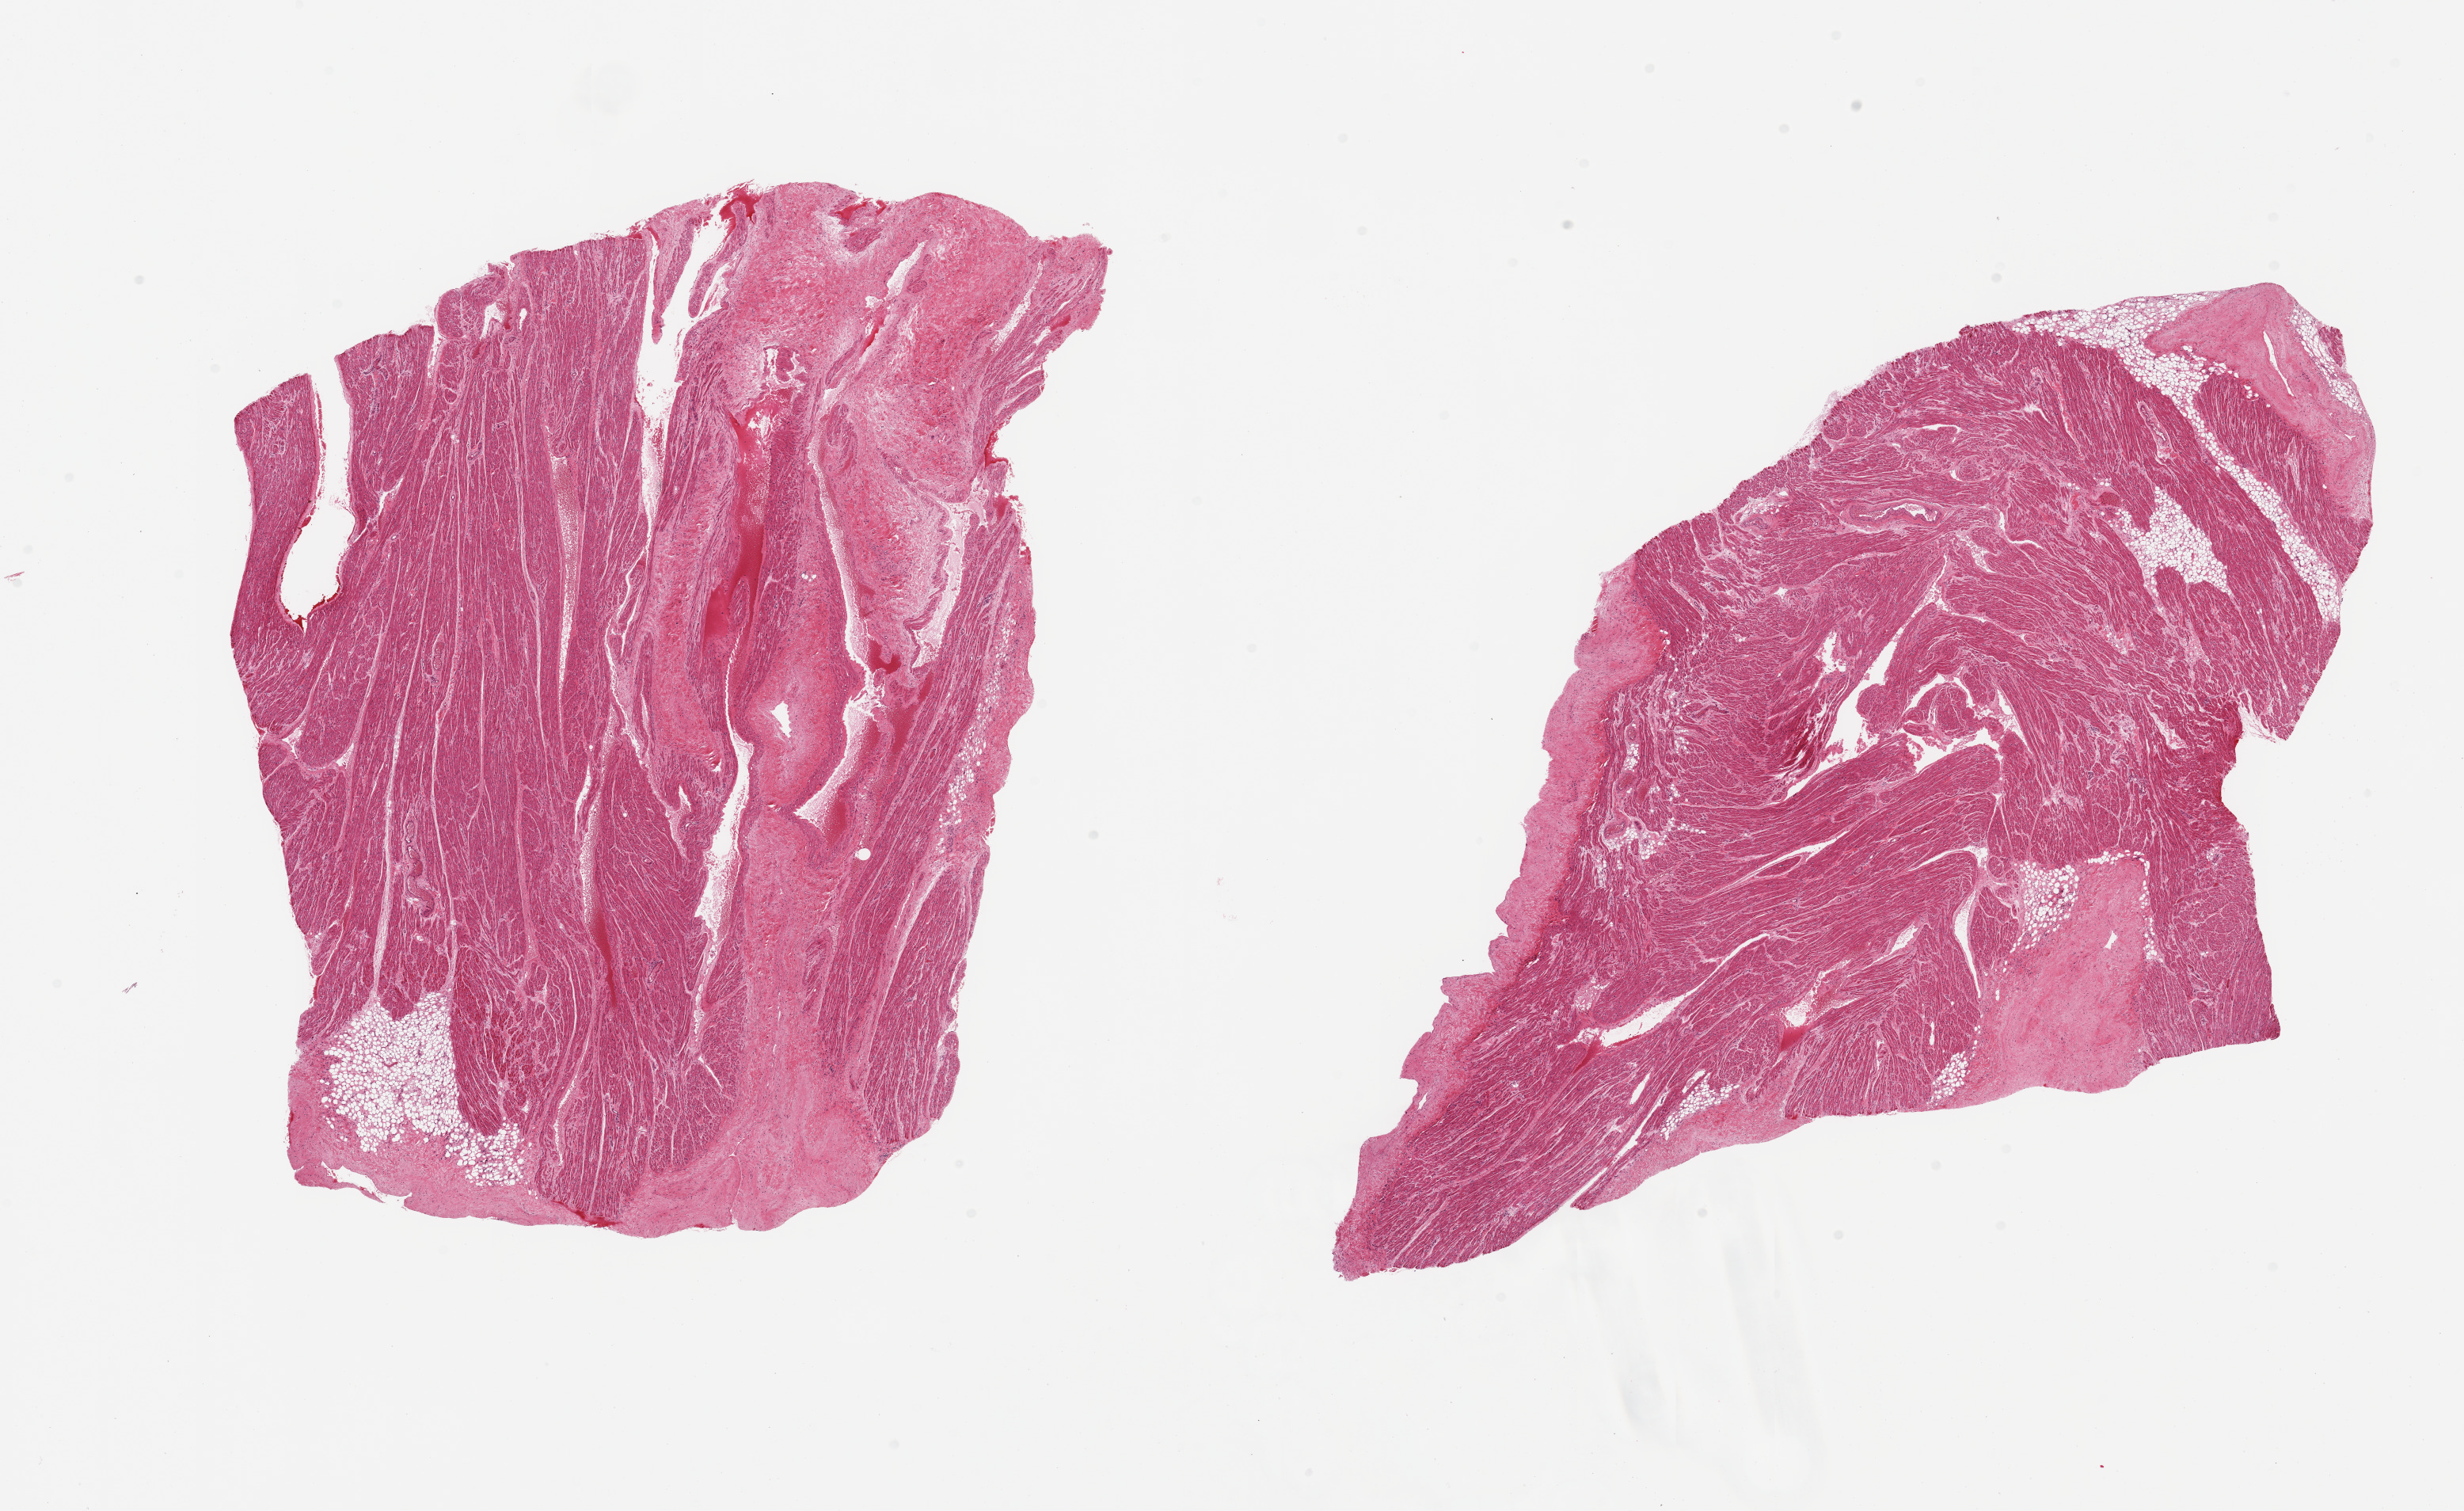
Hematoxylin and eosin (H&E) whole-slide image — low-resolution overview of the scanned area, about 24.6 x 15.1 mm; PAXgene-fixed, paraffin-embedded tissue; section of auricular appendage (target tissue); donor tissue sample. Donor: male.
Reviewer comment on this tissue sample: 2 pieces, no abnormalities.